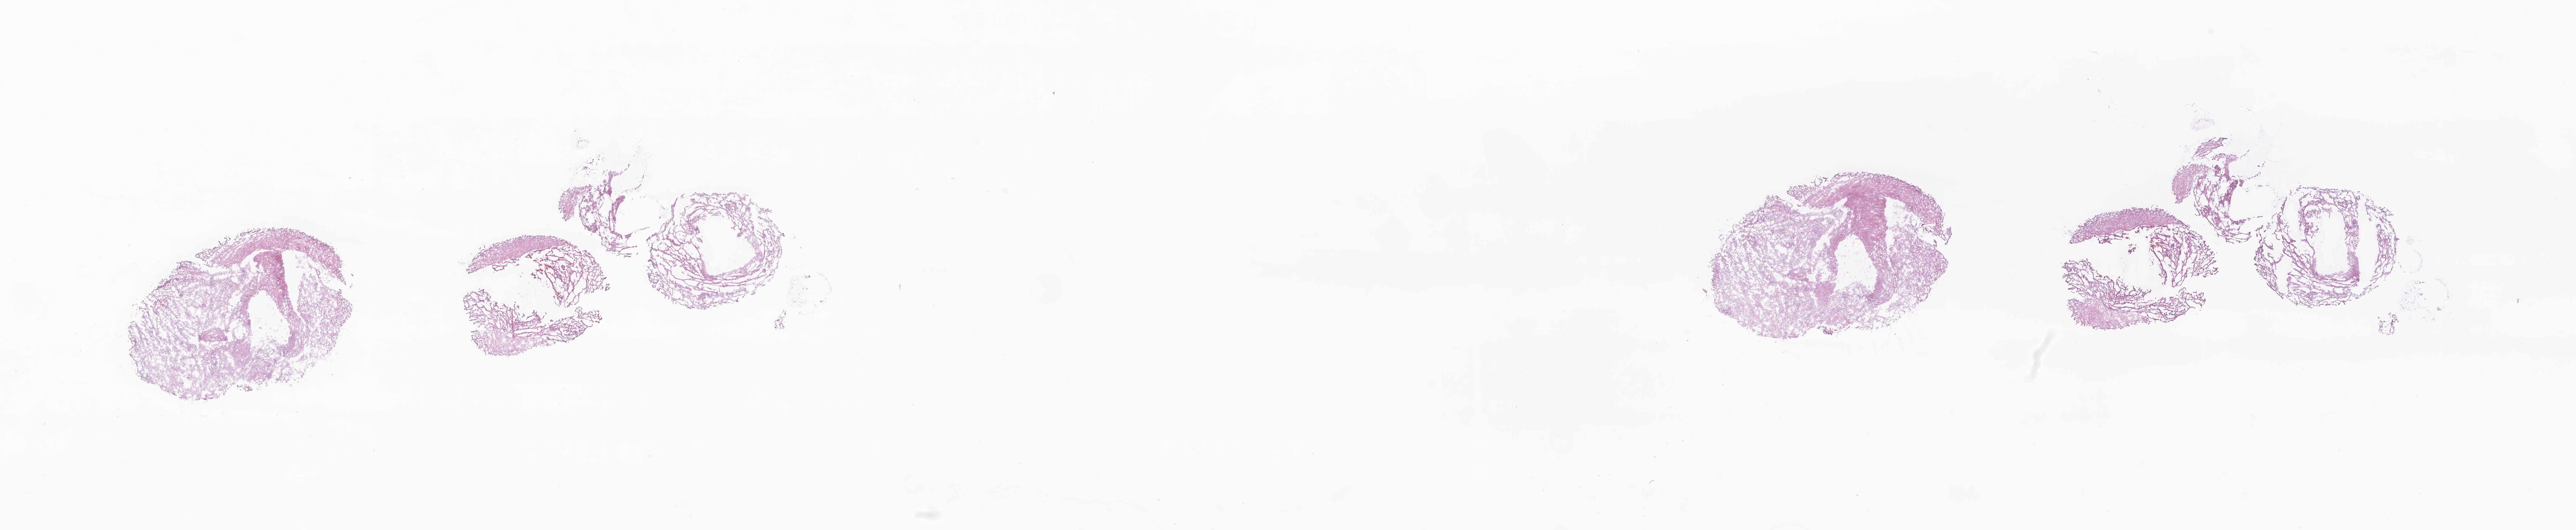
Whole-slide image, hematoxylin and eosin (H&E) stain of tumor tissue from the cerebral ventricle, whole scanned area (about 37.4 x 7.7 mm) shown as a low-resolution overview; cryosection (OCT / tissue freezing medium). Patient female; age 71 months.
Diagnosis (ICD-O-3 morphology term): Pilocytic astrocytoma.